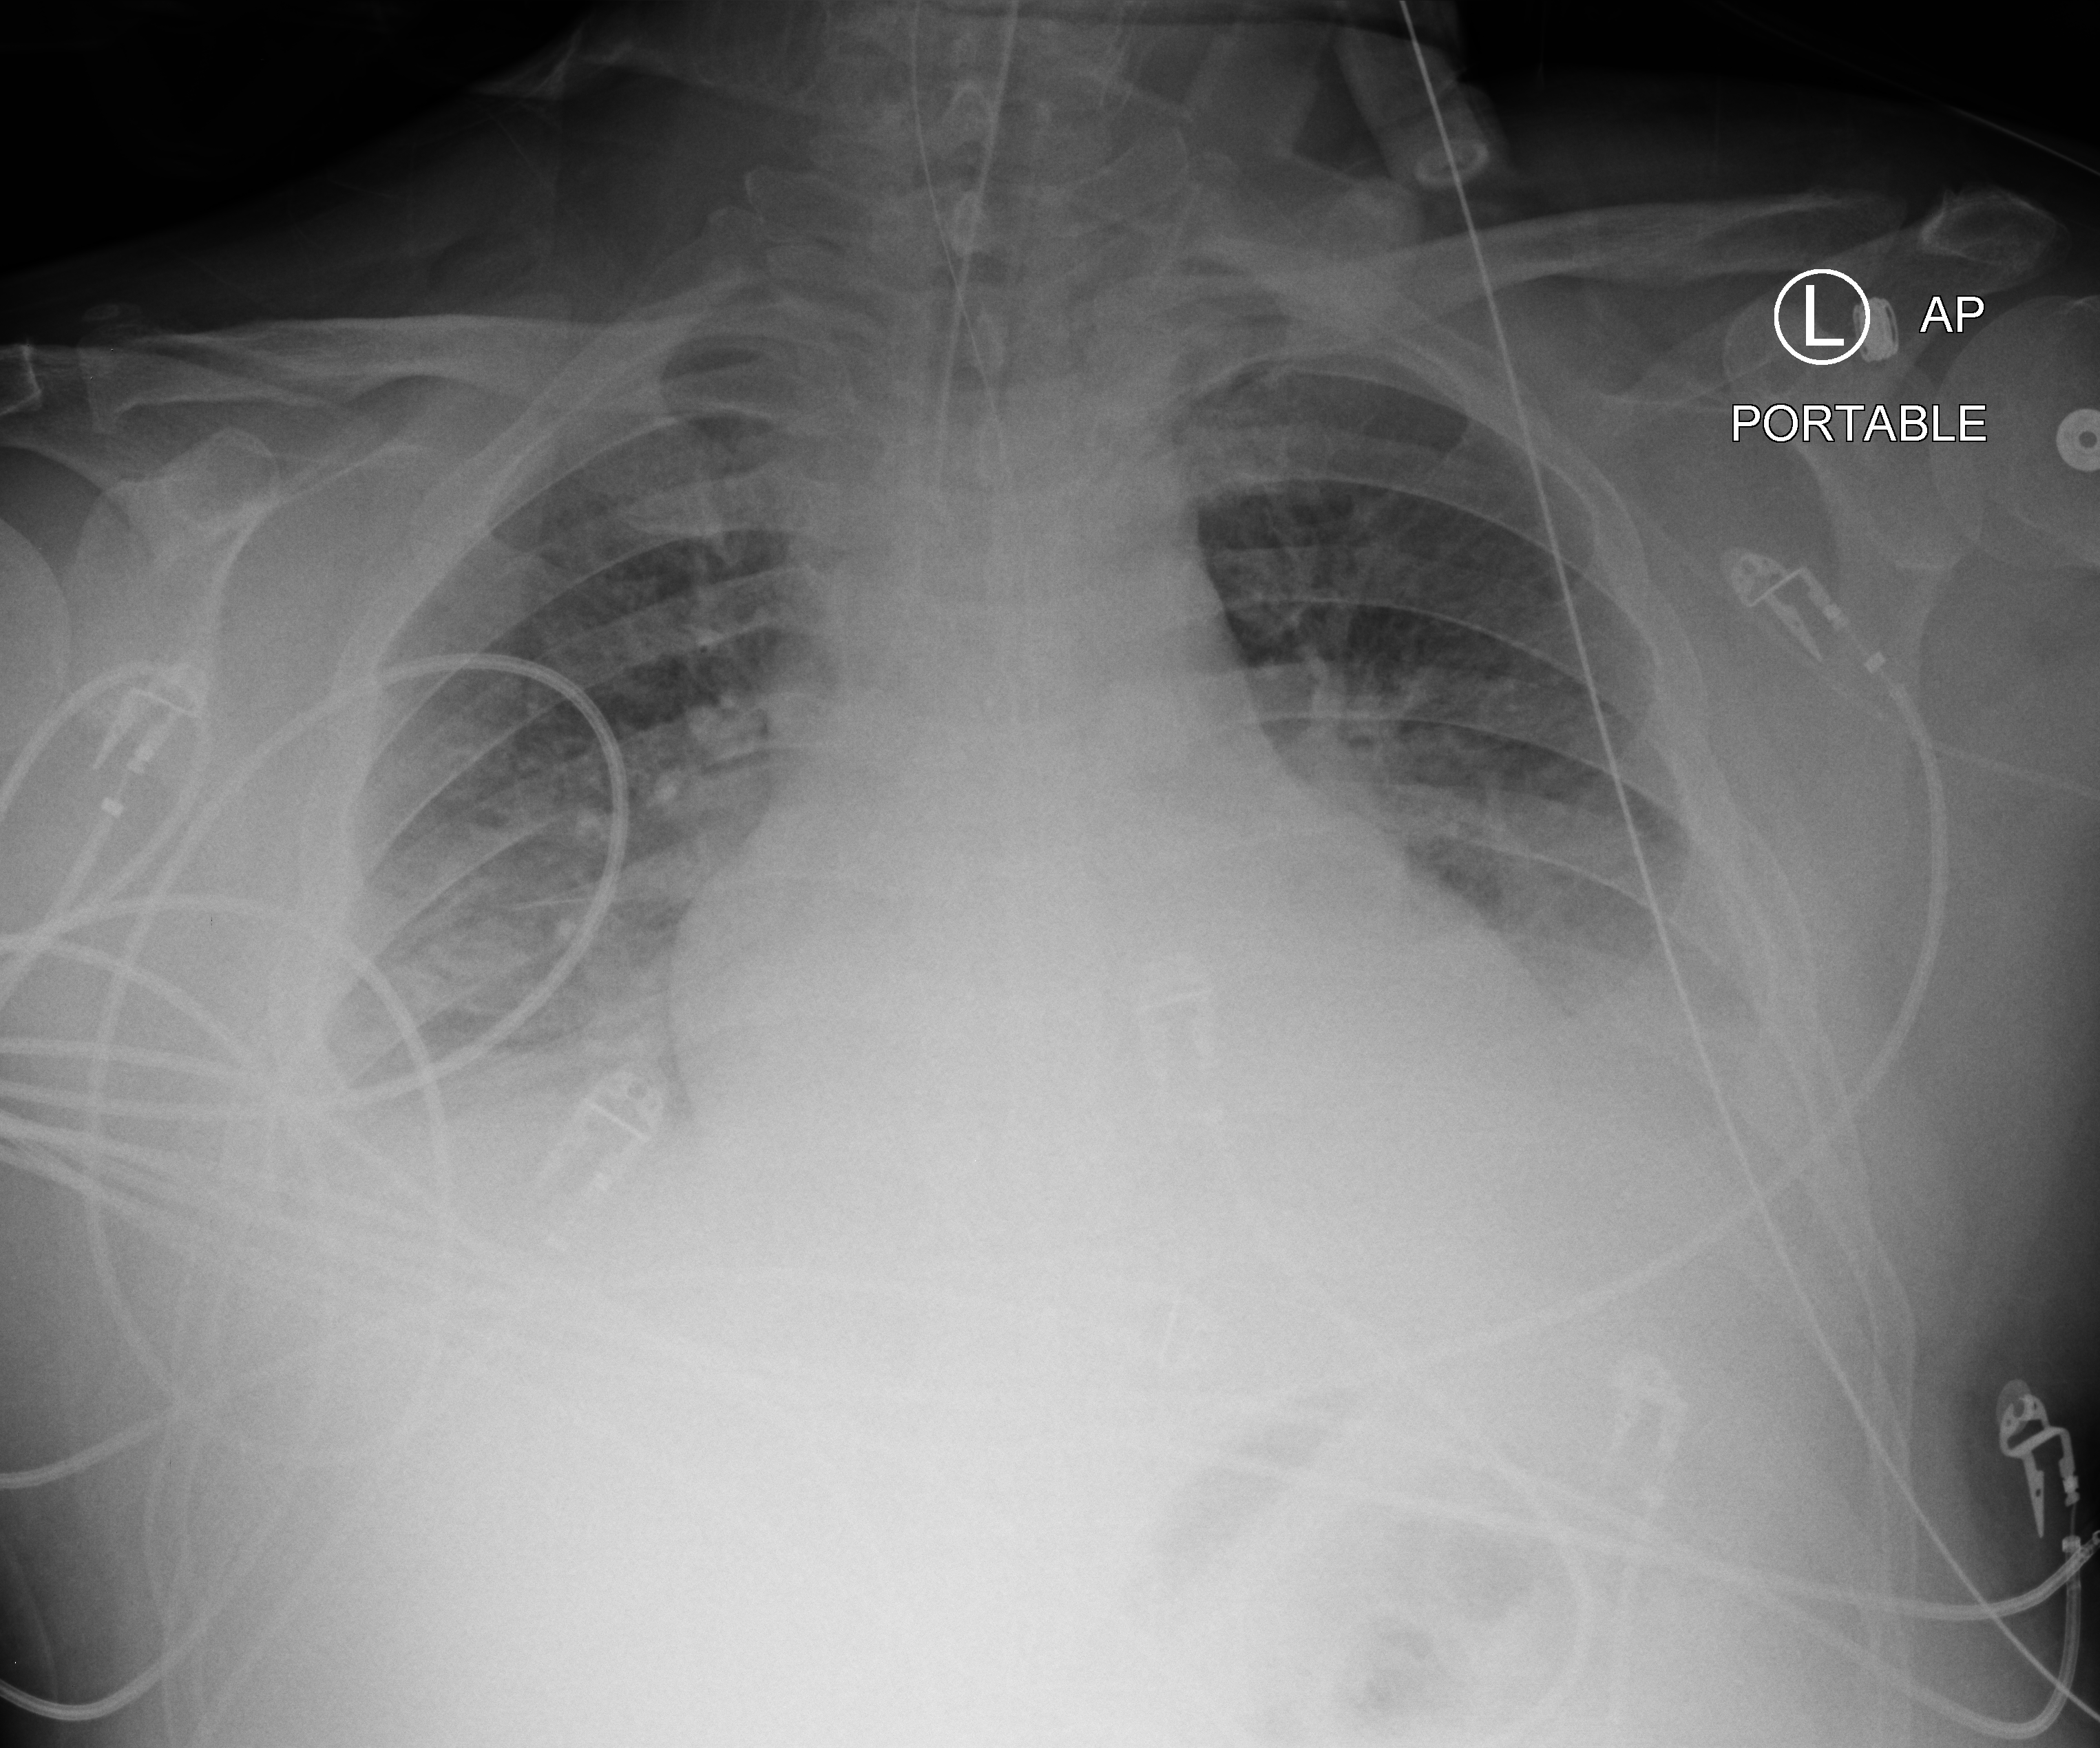
Chest X-ray (portable). Patient hospitalised with COVID-19; male, aged 18–59 years.
Hospital-stay facts (about this admission, not read from this image; timing relative to this image not recorded): admitted to intensive care during this hospital stay: yes.